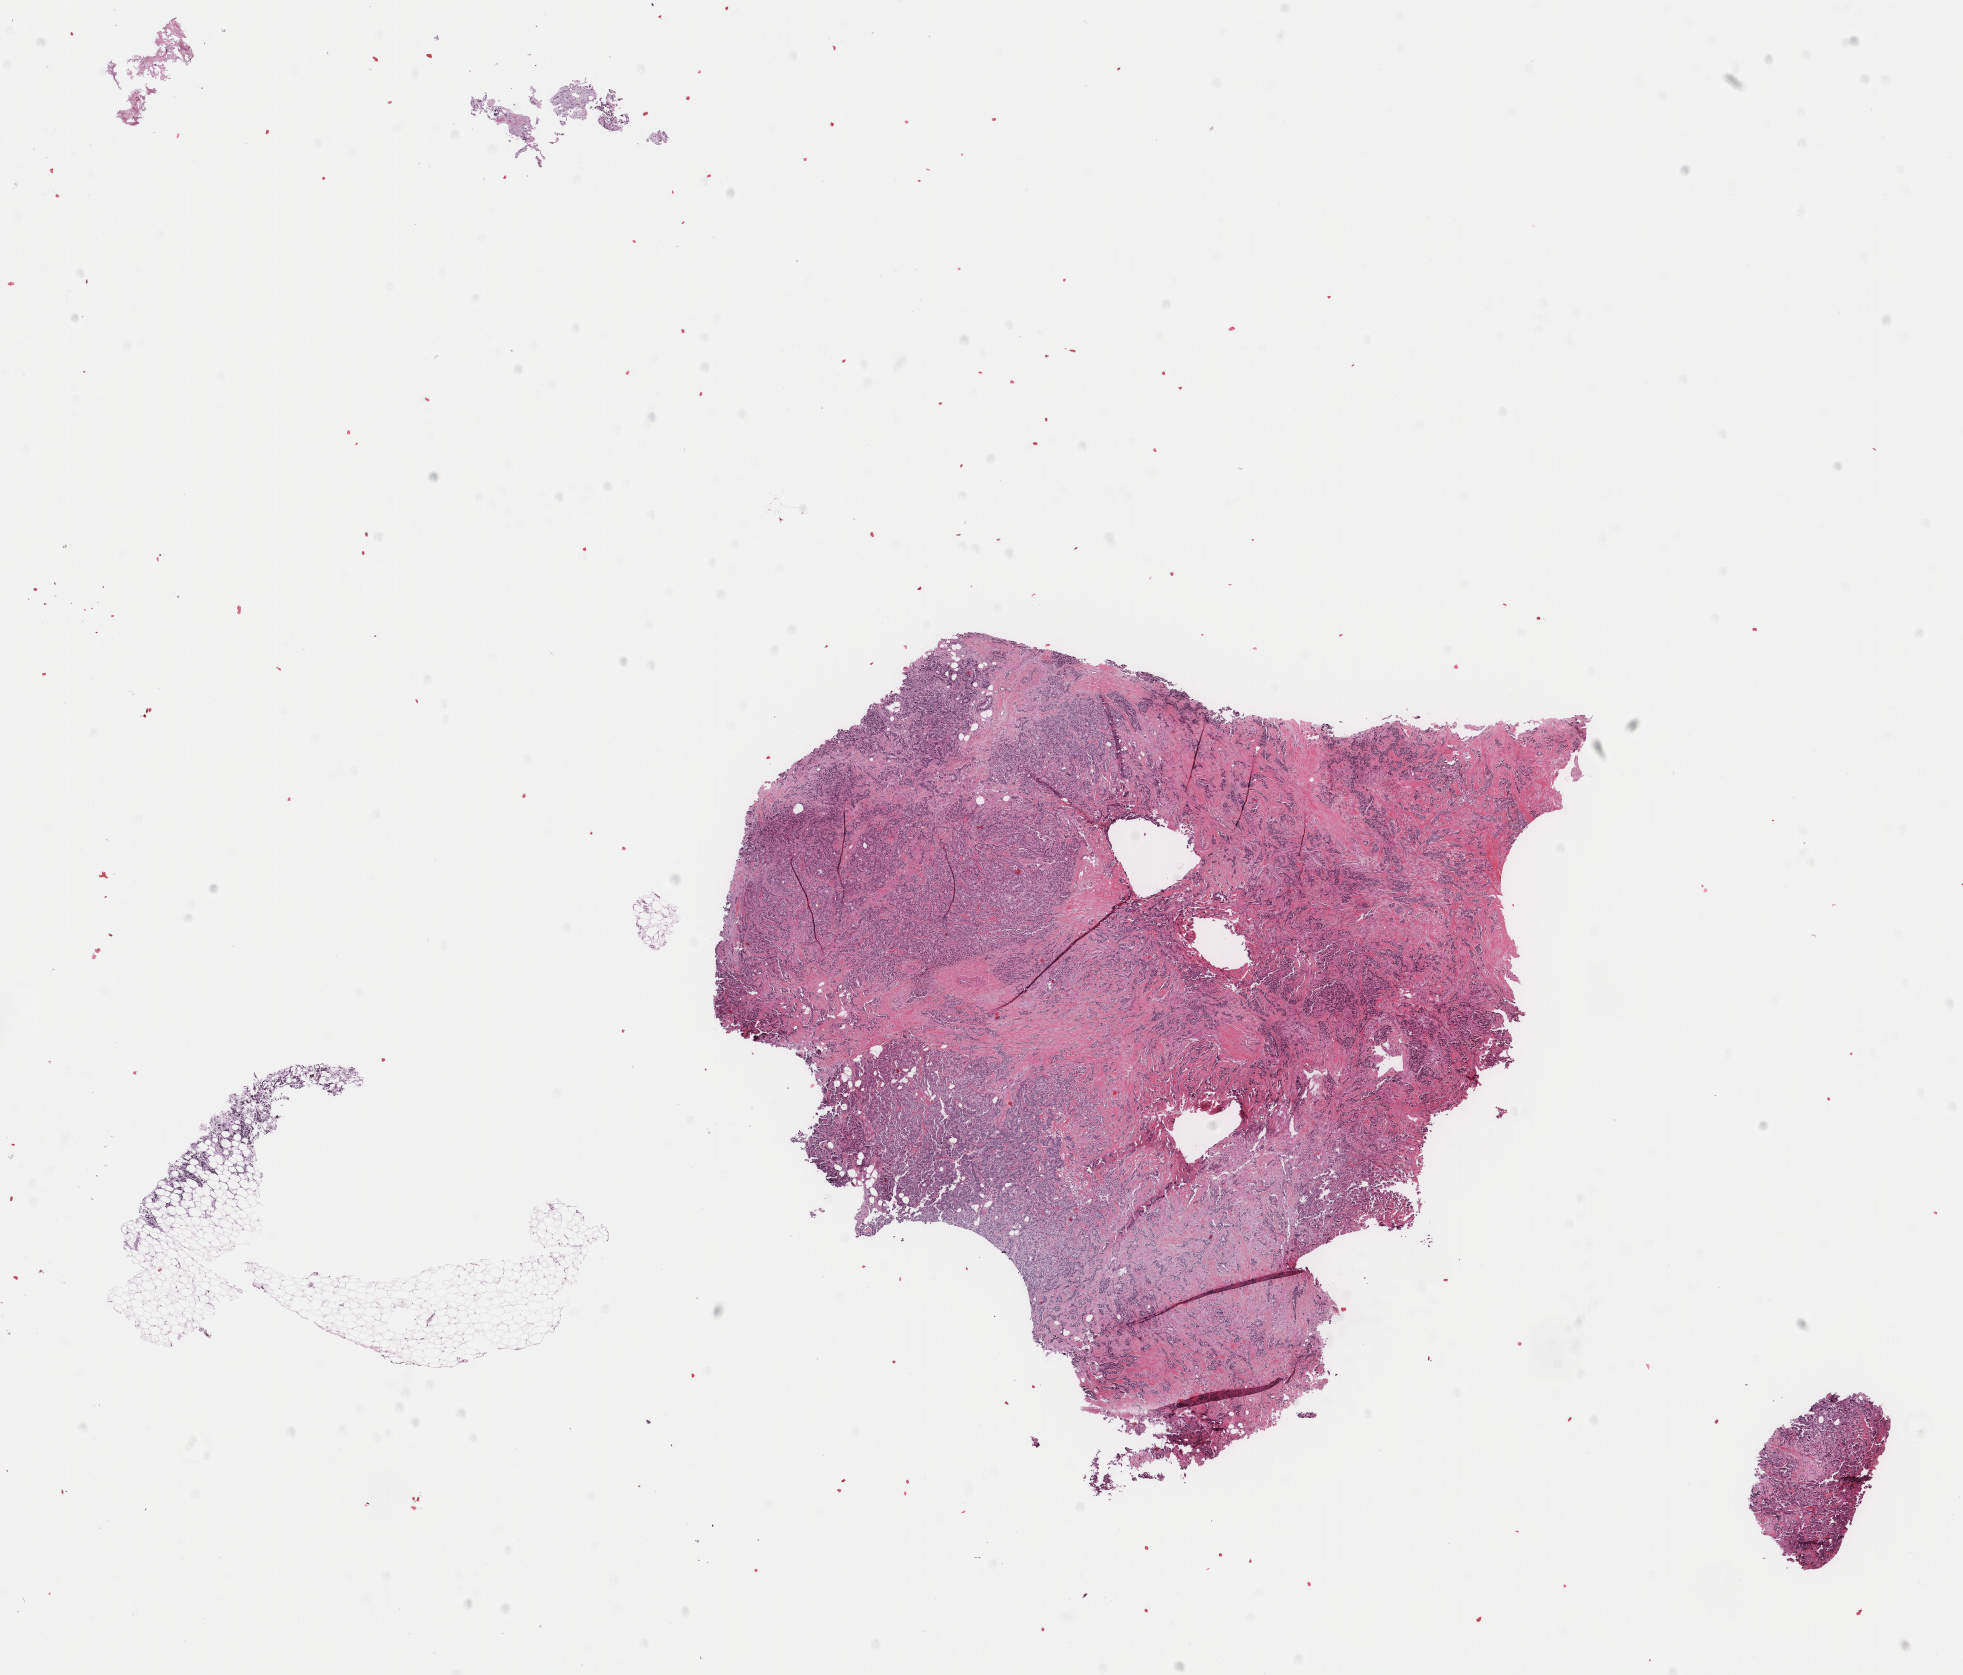
H&E whole-slide image, a low-resolution overview of the entire scanned area, about 15.6 x 13.3 mm (acquisition: 40x scan); FFPE section; primary tumour sample from the breast. Female patient; age at initial diagnosis 57 years.
AJCC pathologic stage: IIA (6th edition). Histologic diagnosis: Infiltrating duct carcinoma, NOS. Lymph nodes positive (case pathology): 0 of 8 examined.